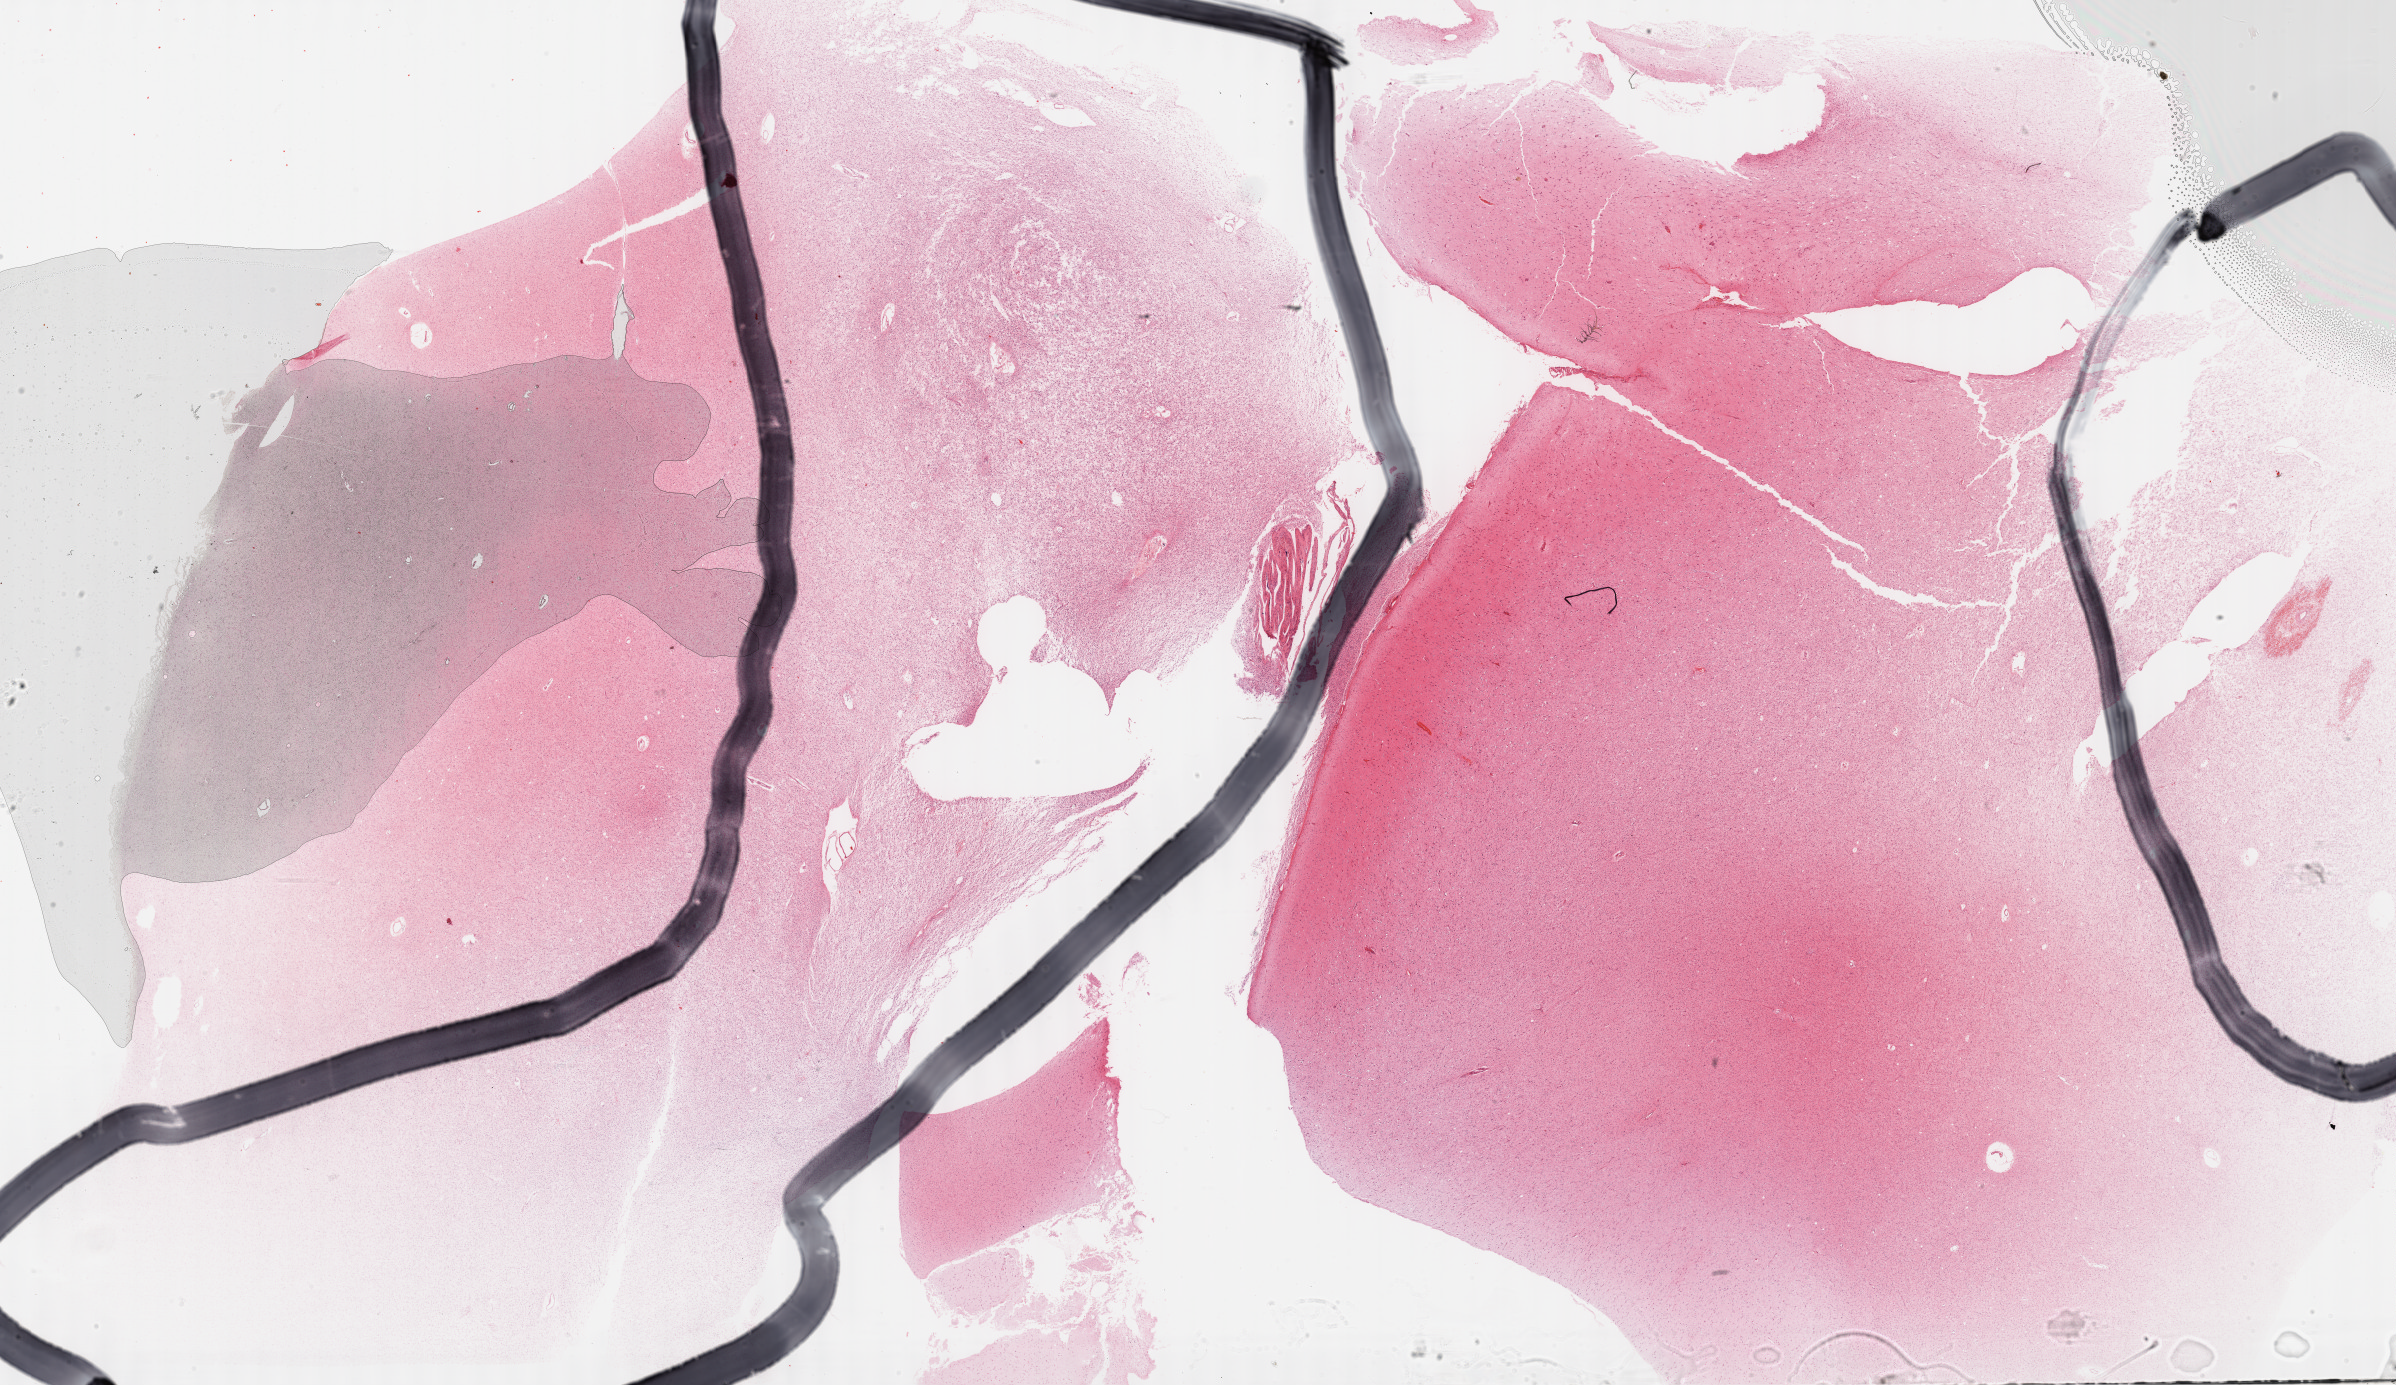
H&E-stained whole-slide image — a low-resolution overview of the entire scanned area, about 38.8 x 22.4 mm, formalin-fixed paraffin-embedded (FFPE) diagnostic section, brain, primary tumour sample. Male, age 24 years at initial diagnosis. Histologic grade: G2 (moderately differentiated).
Laterality: left. Histologic diagnosis: Astrocytoma, NOS.